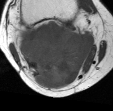
MRI of an extremity soft-tissue mass, one axial slice; position 24 of 45 along the scan axis; MR volume resampled by the dataset authors to the PET/CT grid (not the native acquisition matrix); 3.27 mm slice thickness; 113 × 111 image matrix, field of view 110 × 108 mm. Female patient. Case-level facts recorded for this patient, not image findings: histological type: liposarcoma; site of the primary tumour: right thigh.
Structures marked on this image (expert contour drawn on MRI and transferred to this co-registered scan by the dataset authors):
- gross tumour volume (mass): bounding box (x1, y1, x2, y2) in pixels: (17, 20, 98, 89)